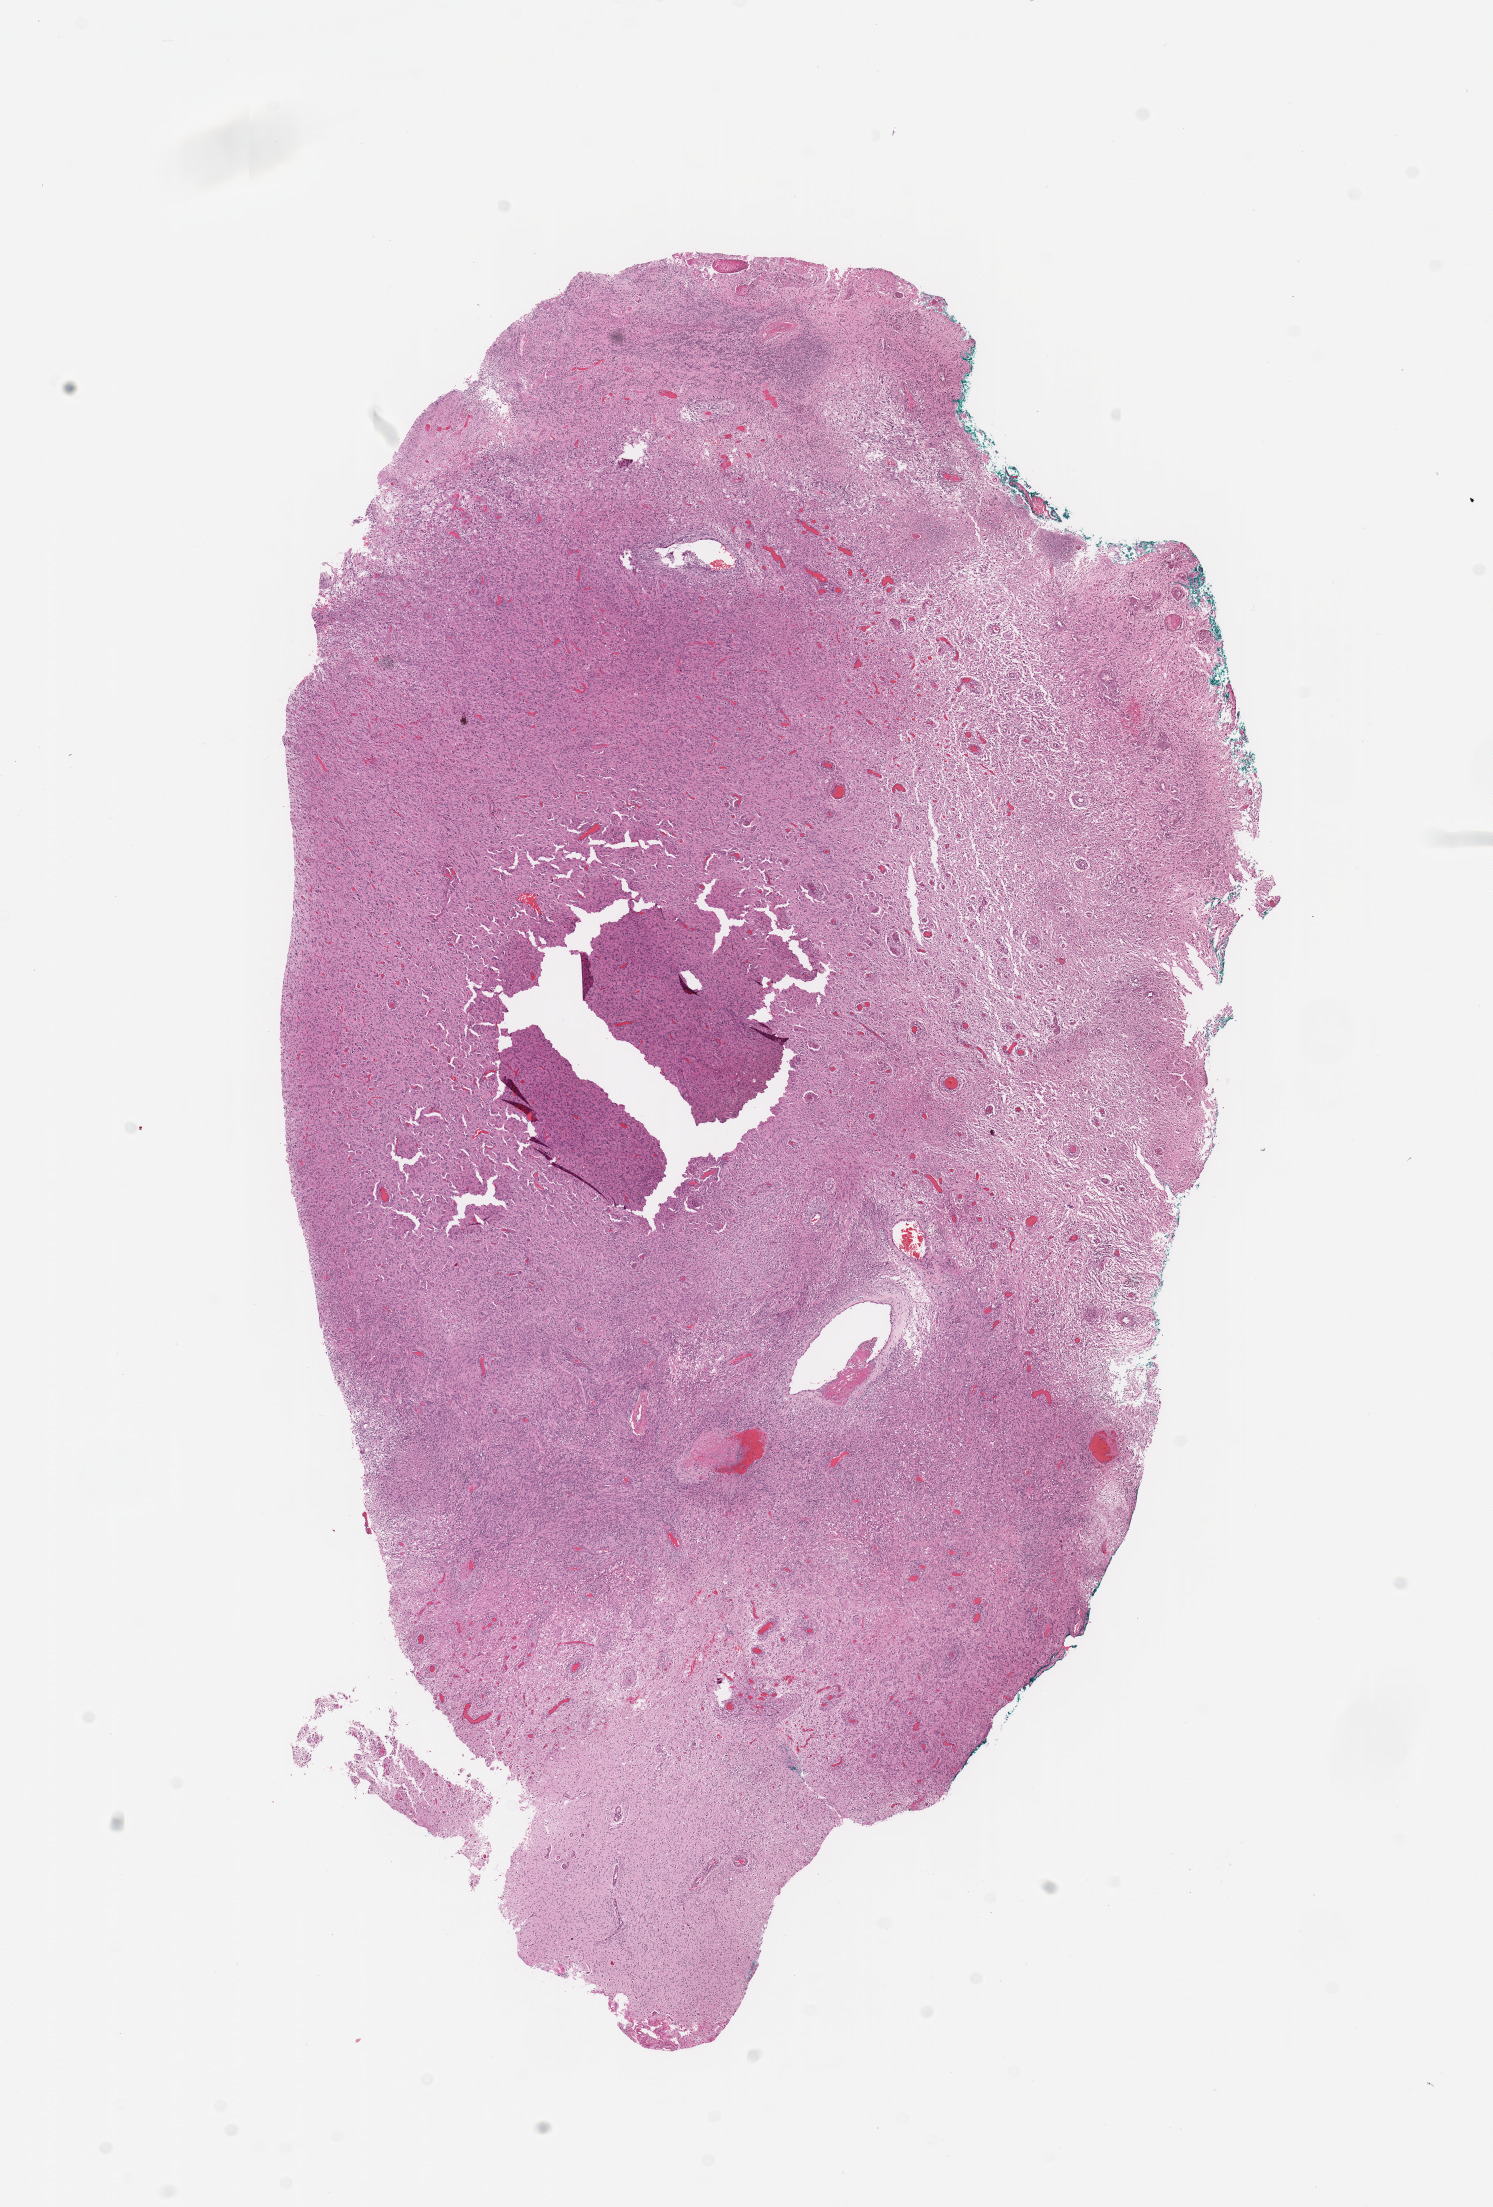
Whole-slide histology image, H&E — a low-resolution overview of the entire scanned area, about 11.8 x 17.5 mm (slide scanned at 20x); brain, tumour tissue. Female, 66 y/o.
• histologic diagnosis: Glioblastoma